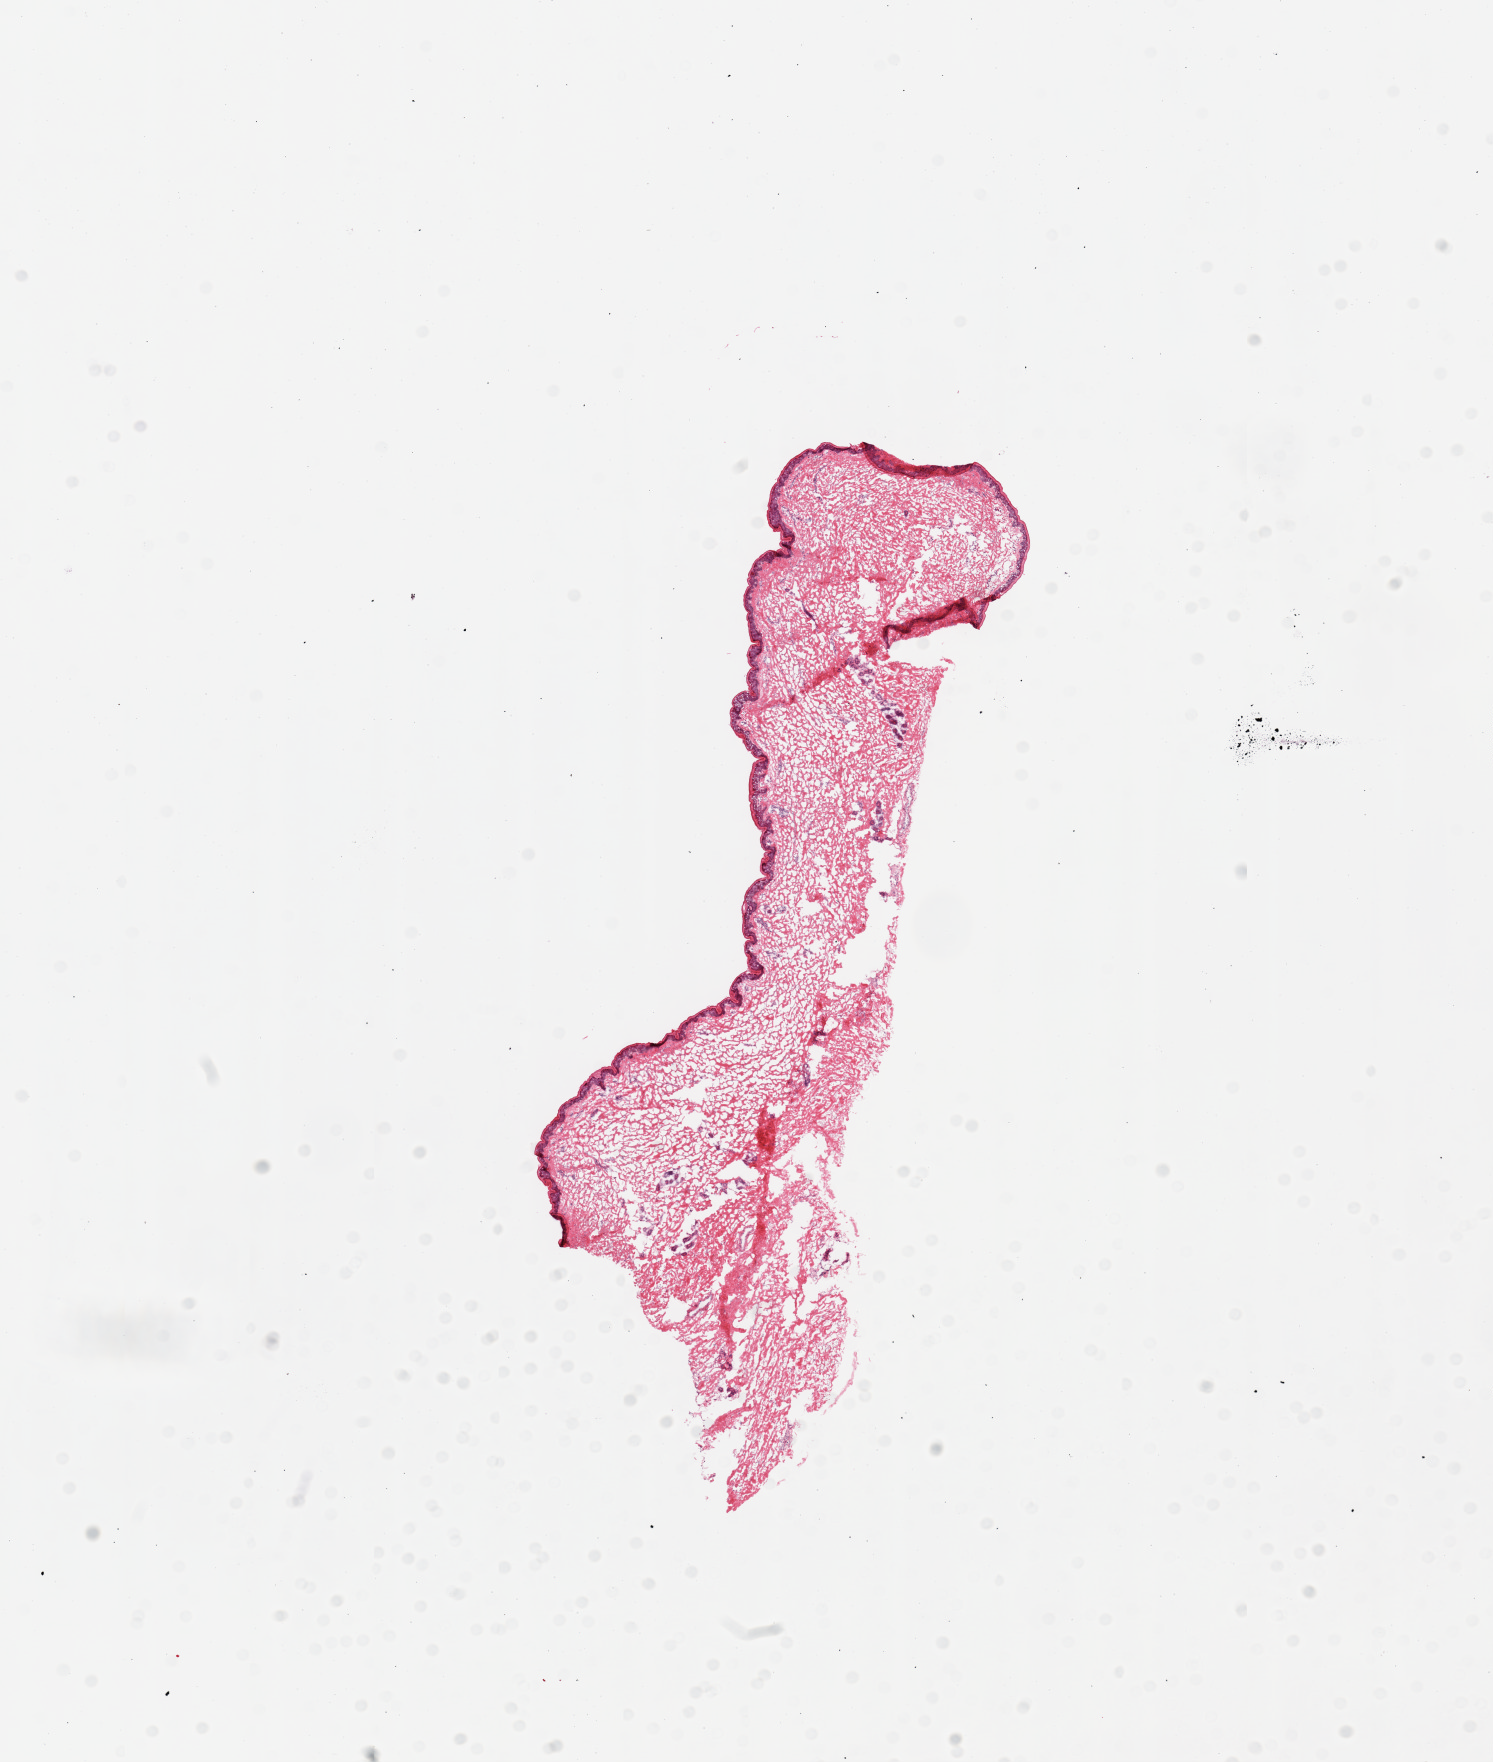
Whole-slide image, hematoxylin and eosin (H&E) stain, brightfield, whole scanned area (about 11.8 x 13.9 mm) shown as a low-resolution overview. Female donor.
• specimen: frozen section (dry ice); sampled site (target tissue): skin of lower leg; donor tissue sample